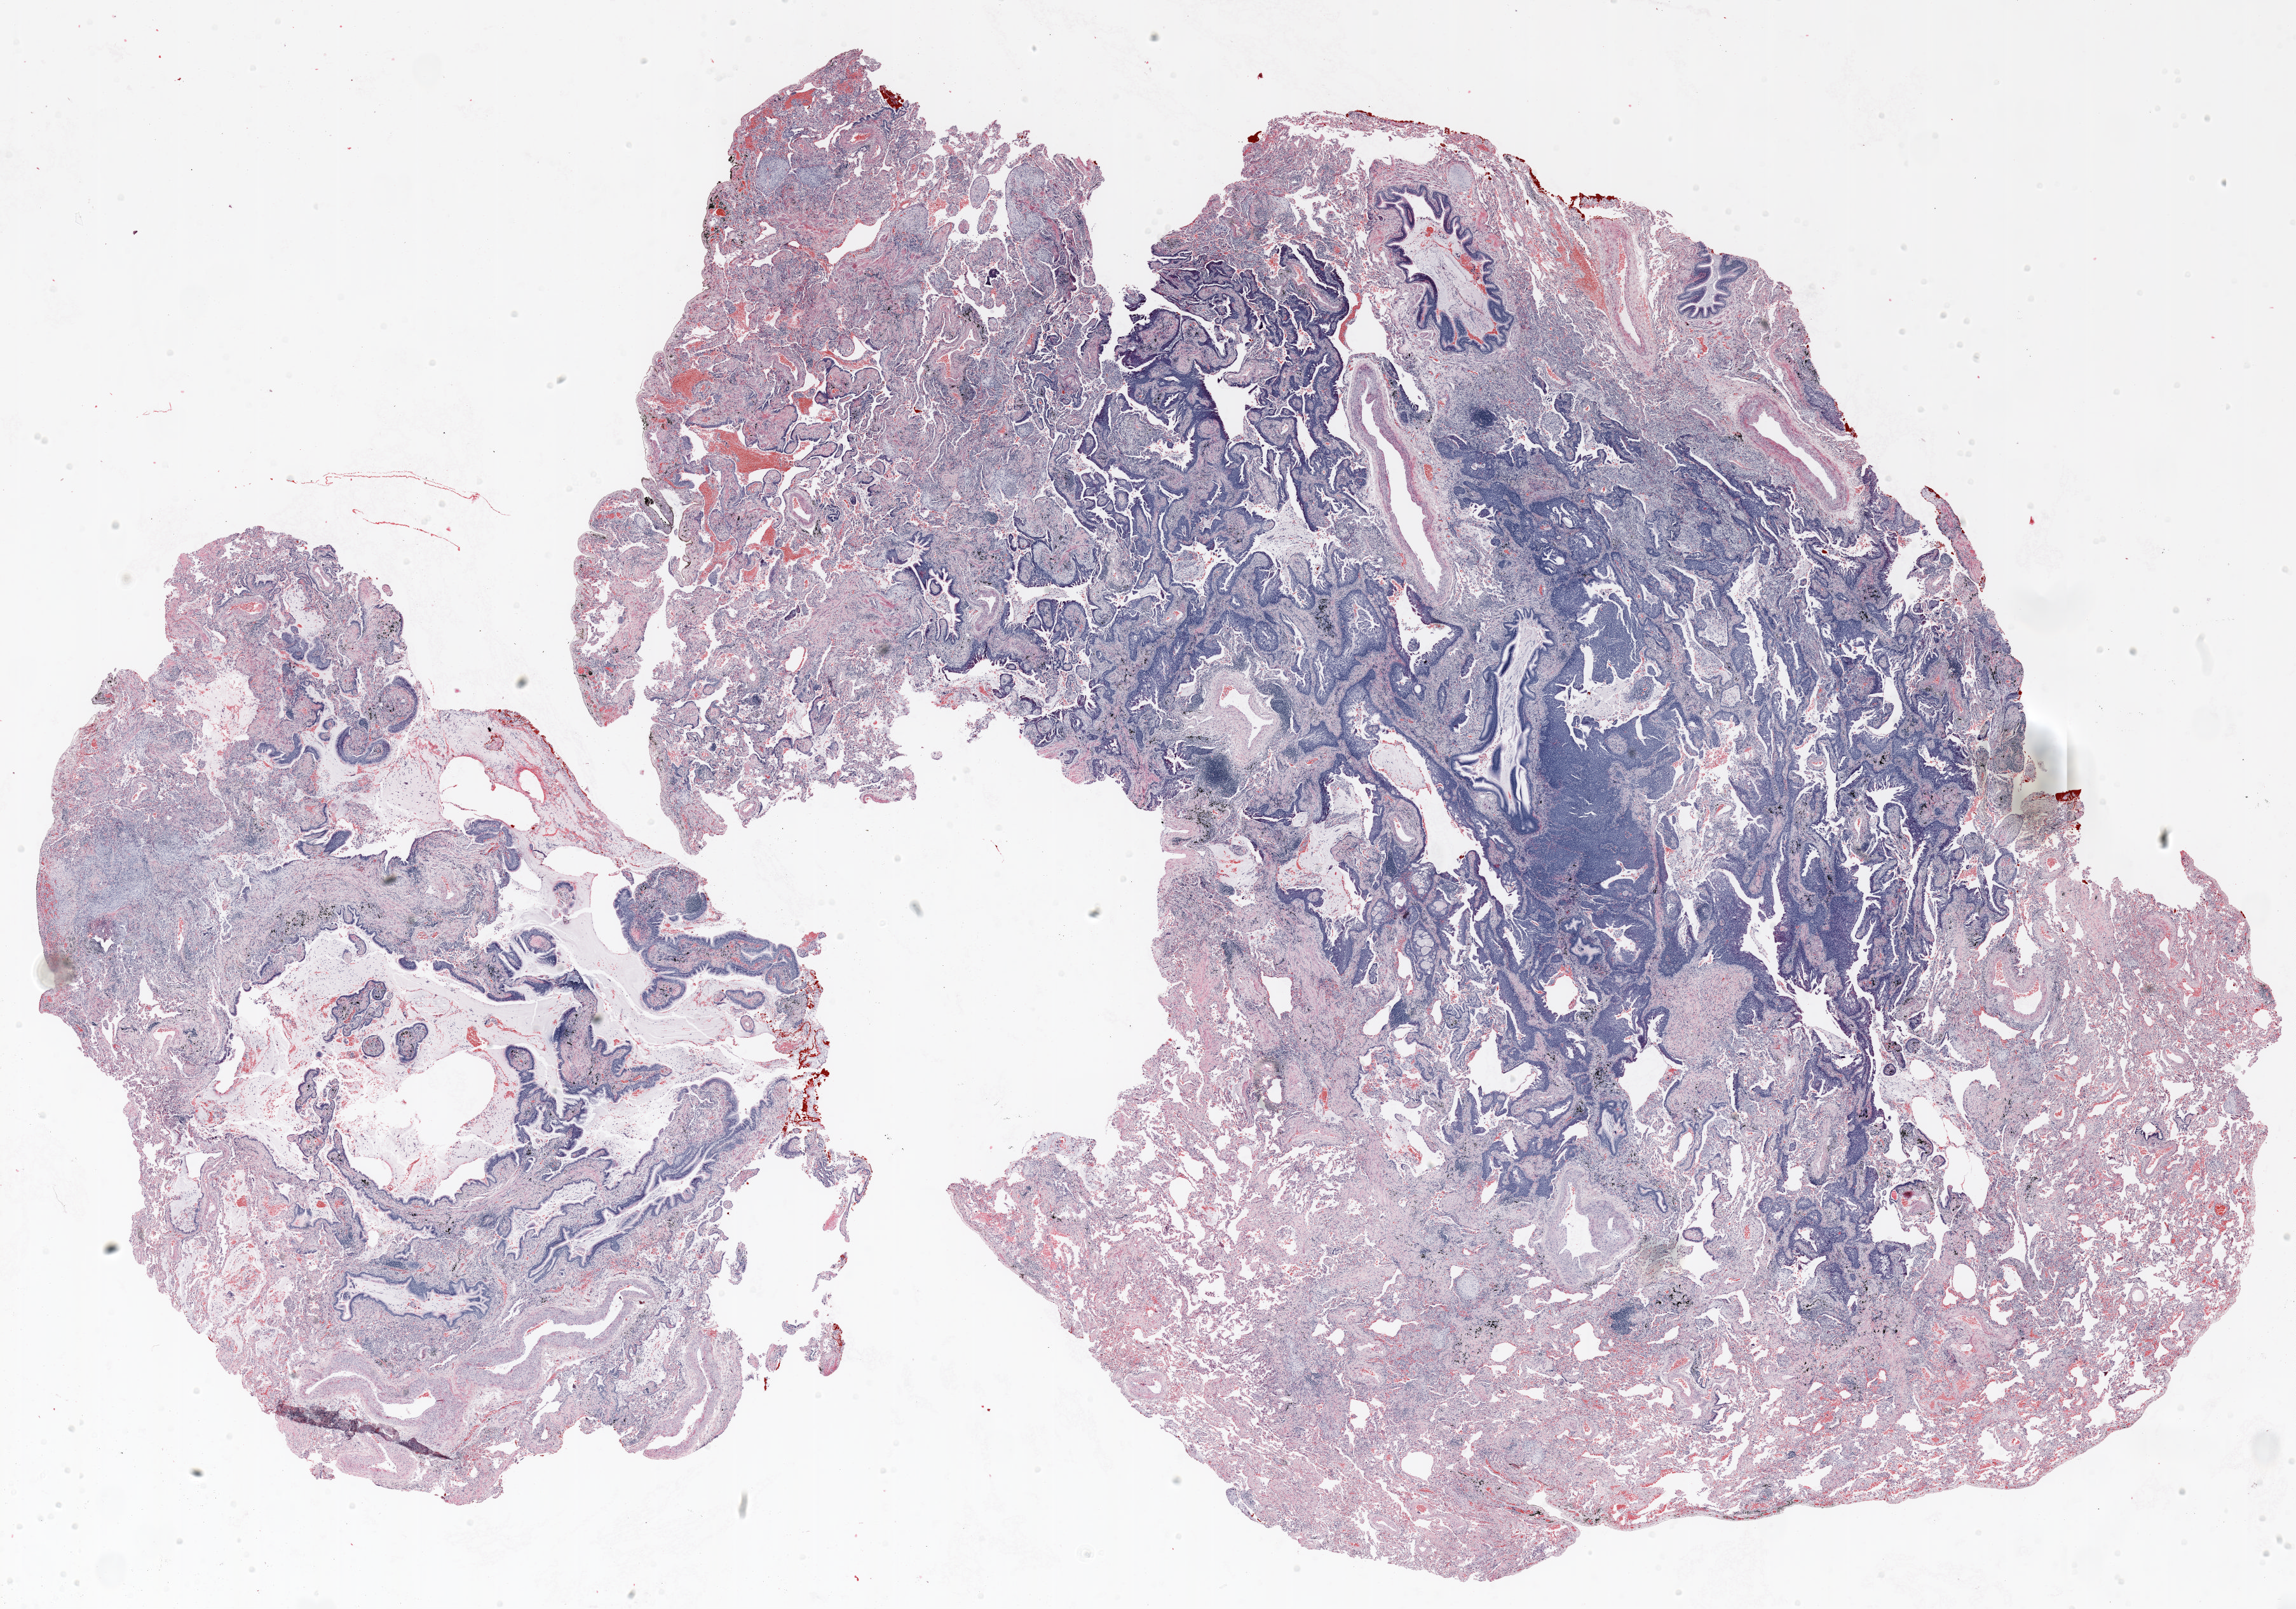
Hematoxylin and eosin (H&E) stained whole-slide image, whole scanned area (about 29.0 x 20.3 mm) shown as a low-resolution overview. Formalin-fixed paraffin-embedded (FFPE) section. Lung. Male patient, aged 67 at enrolment. Former smoker at enrolment. Grade: moderately differentiated (G2).
Primary tumour location (clinical record): right lower lobe. Participant's lung-cancer diagnosis: Squamous cell carcinoma, NOS (ICD-O-3 8070/3). Tumour size (pathology): 23 mm. Stage (AJCC 6th edition): IA.